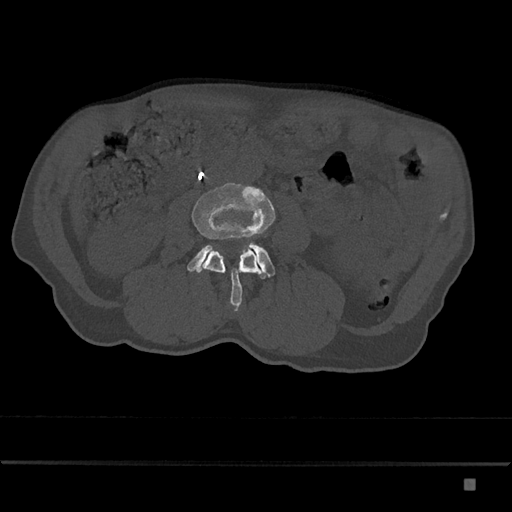
CT including the spine, one axial slice; position 380 of 797 along the scan axis; reconstruction kernel Br40s/3; 120 kVp; bone window (W 1800 / L 400 HU); 0.5 mm slice thickness; 512 × 512 image matrix. Patient: male, 72 years. From the clinical record (not read from this slice): primary cancer: prostate.
Outlined on this slice (semi-automatic segmentation, software-assisted and operator-edited):
- L3 vertebra: bounding box (x1, y1, x2, y2) in pixels: (192, 181, 276, 312)
- L4 vertebra: (187, 242, 275, 279)